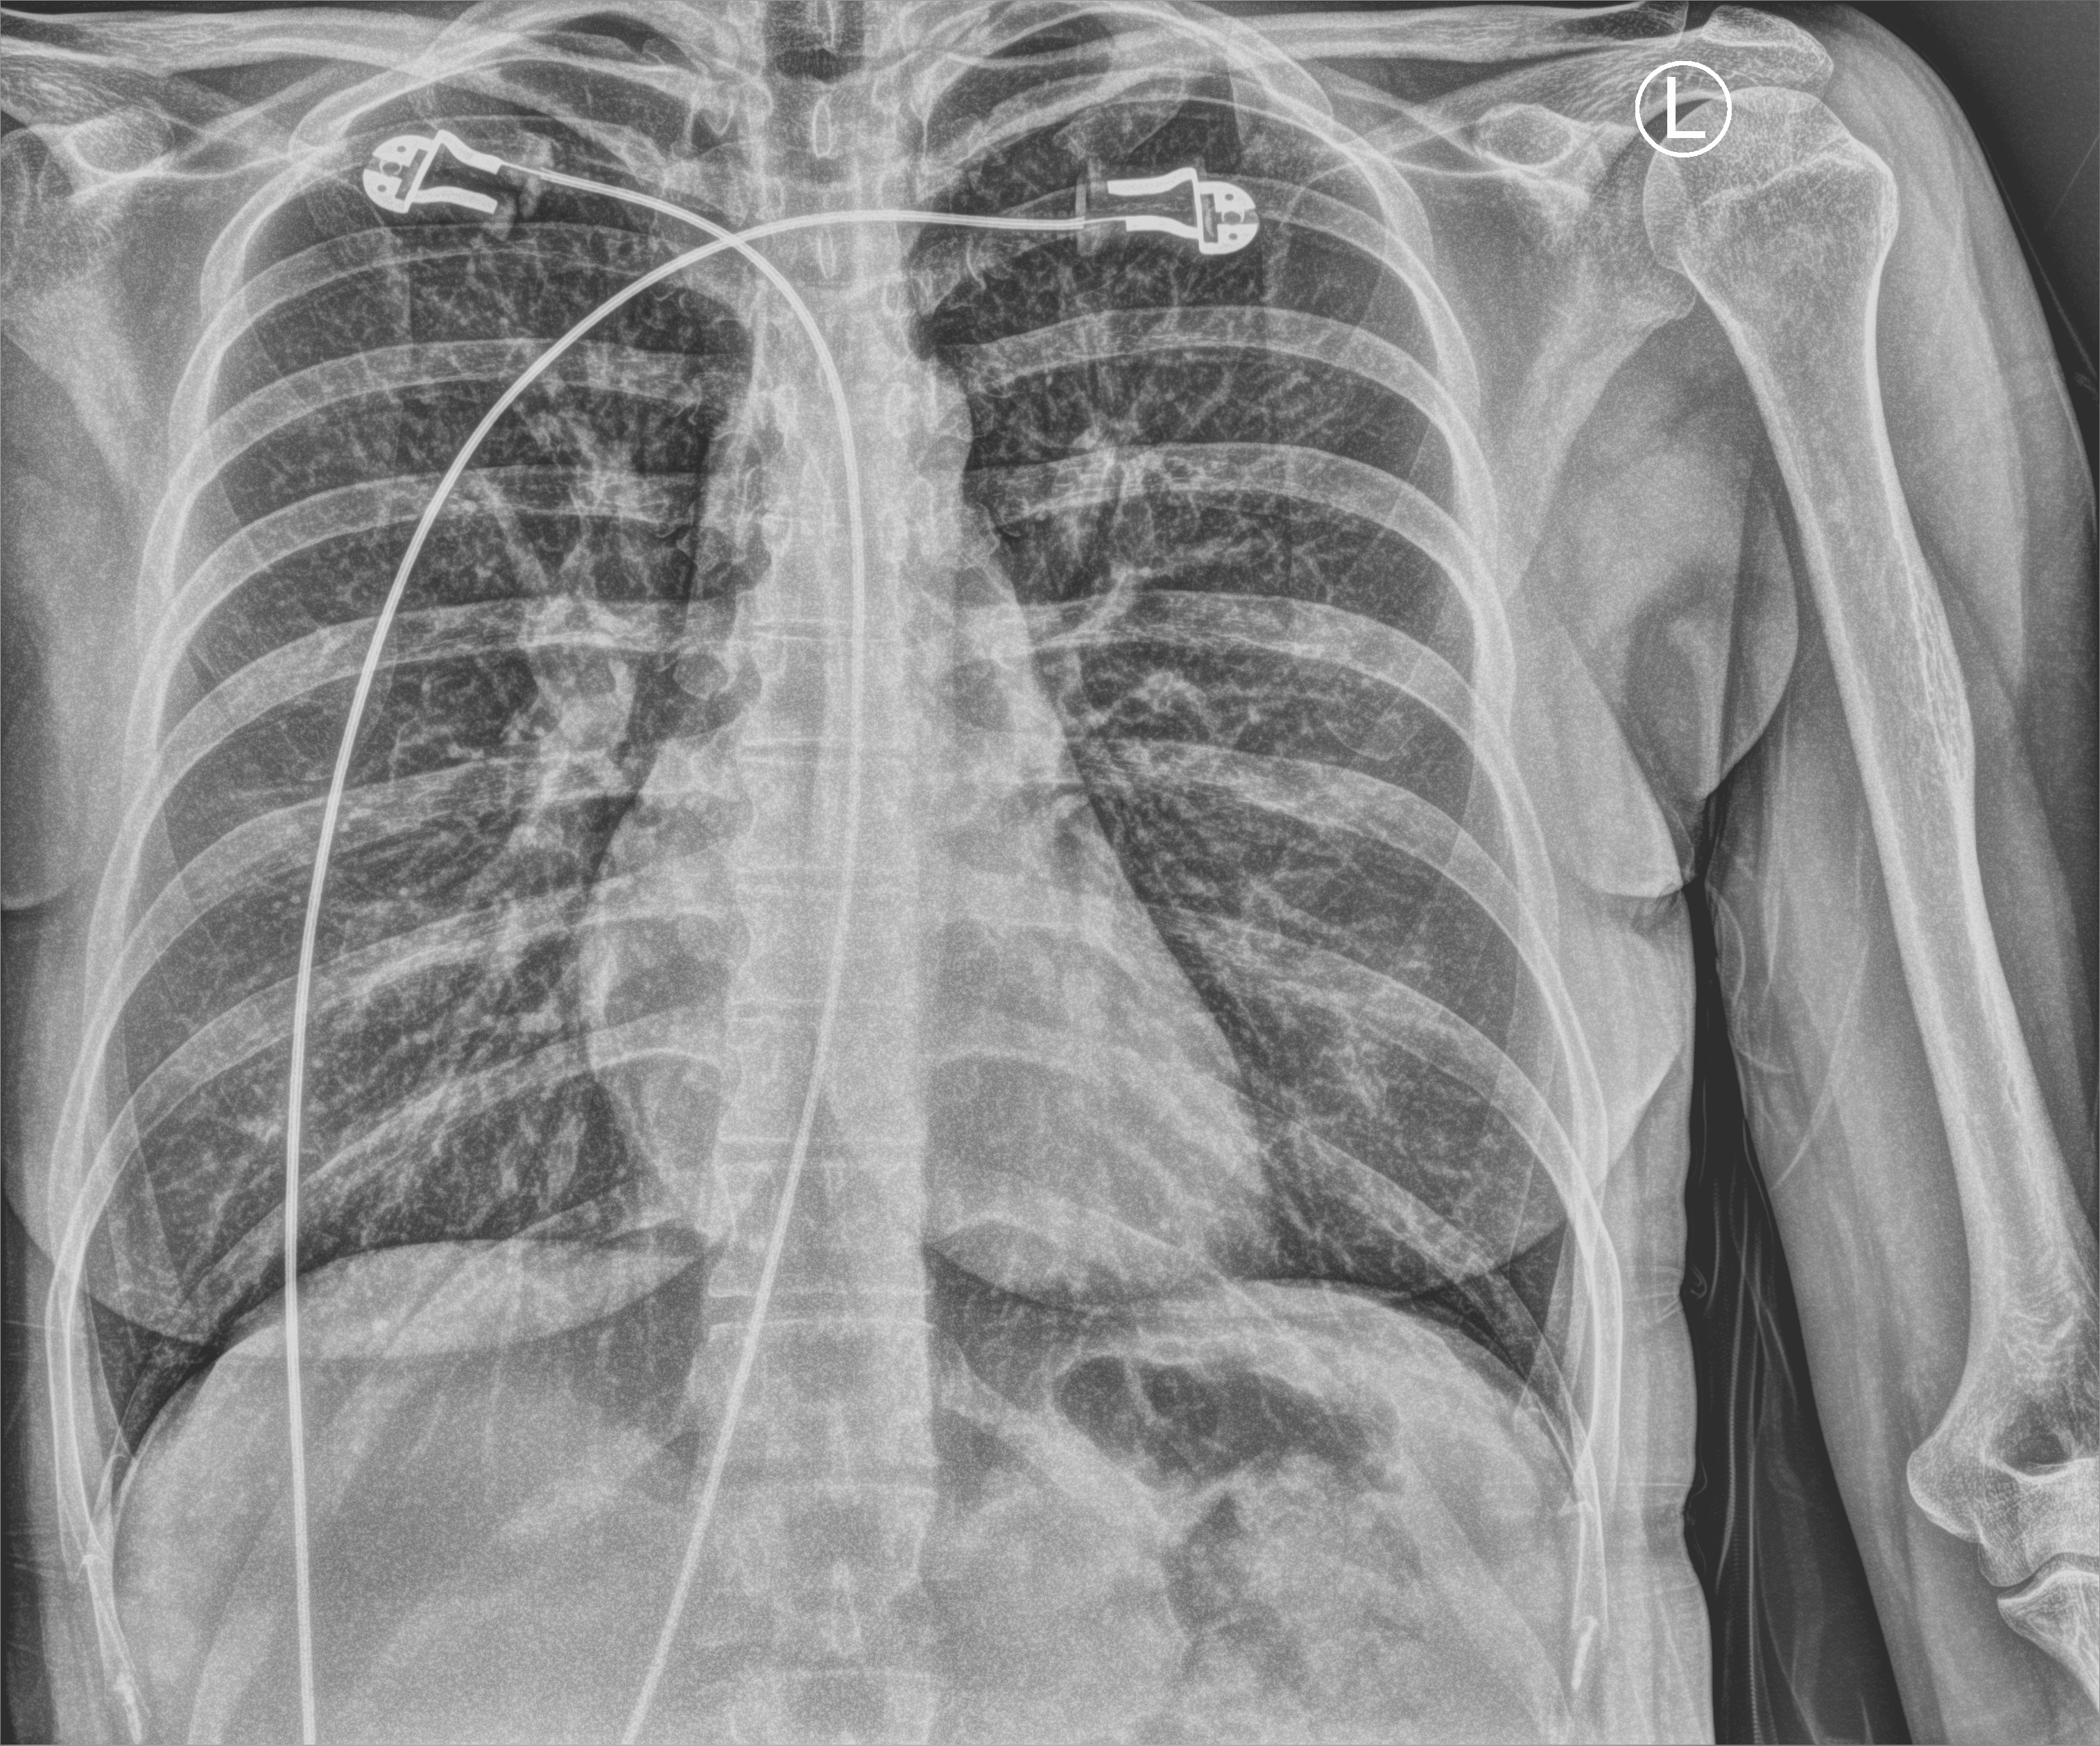
Chest X-ray (portable); anteroposterior (AP) projection. Patient hospitalised with COVID-19; female, aged 18–59 years.
From the hospital-stay record, not from the radiograph (when in the stay this image was taken is not recorded): mechanically ventilated during this hospital stay: no.